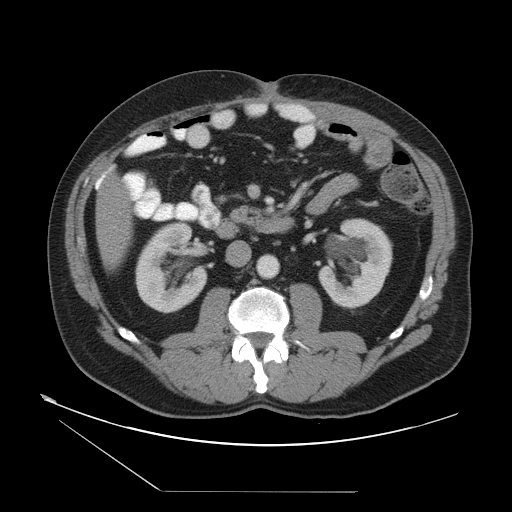
Contrast-enhanced abdominal CT, one axial slice; position 15 of 55 along the scan axis; 120 kVp; intravenous contrast given; soft-tissue window (W 400 / L 40 HU); 5 mm slice thickness; 512 × 512 image matrix, field of view 454 × 454 mm. Male patient, age 59 years. From the clinical record (not read from this slice): diagnosis: colorectal cancer liver metastases, imaged before liver resection; multiple liver metastases: yes; largest metastasis: 0.3 cm; disease in both lobes: yes.
Outlined on this slice (expert manual segmentation):
- liver: bounding box <96,176,133,265> (left, top, right, bottom; pixels)
- planned liver remnant (the part of the liver to remain after resection): <96,176,133,264>